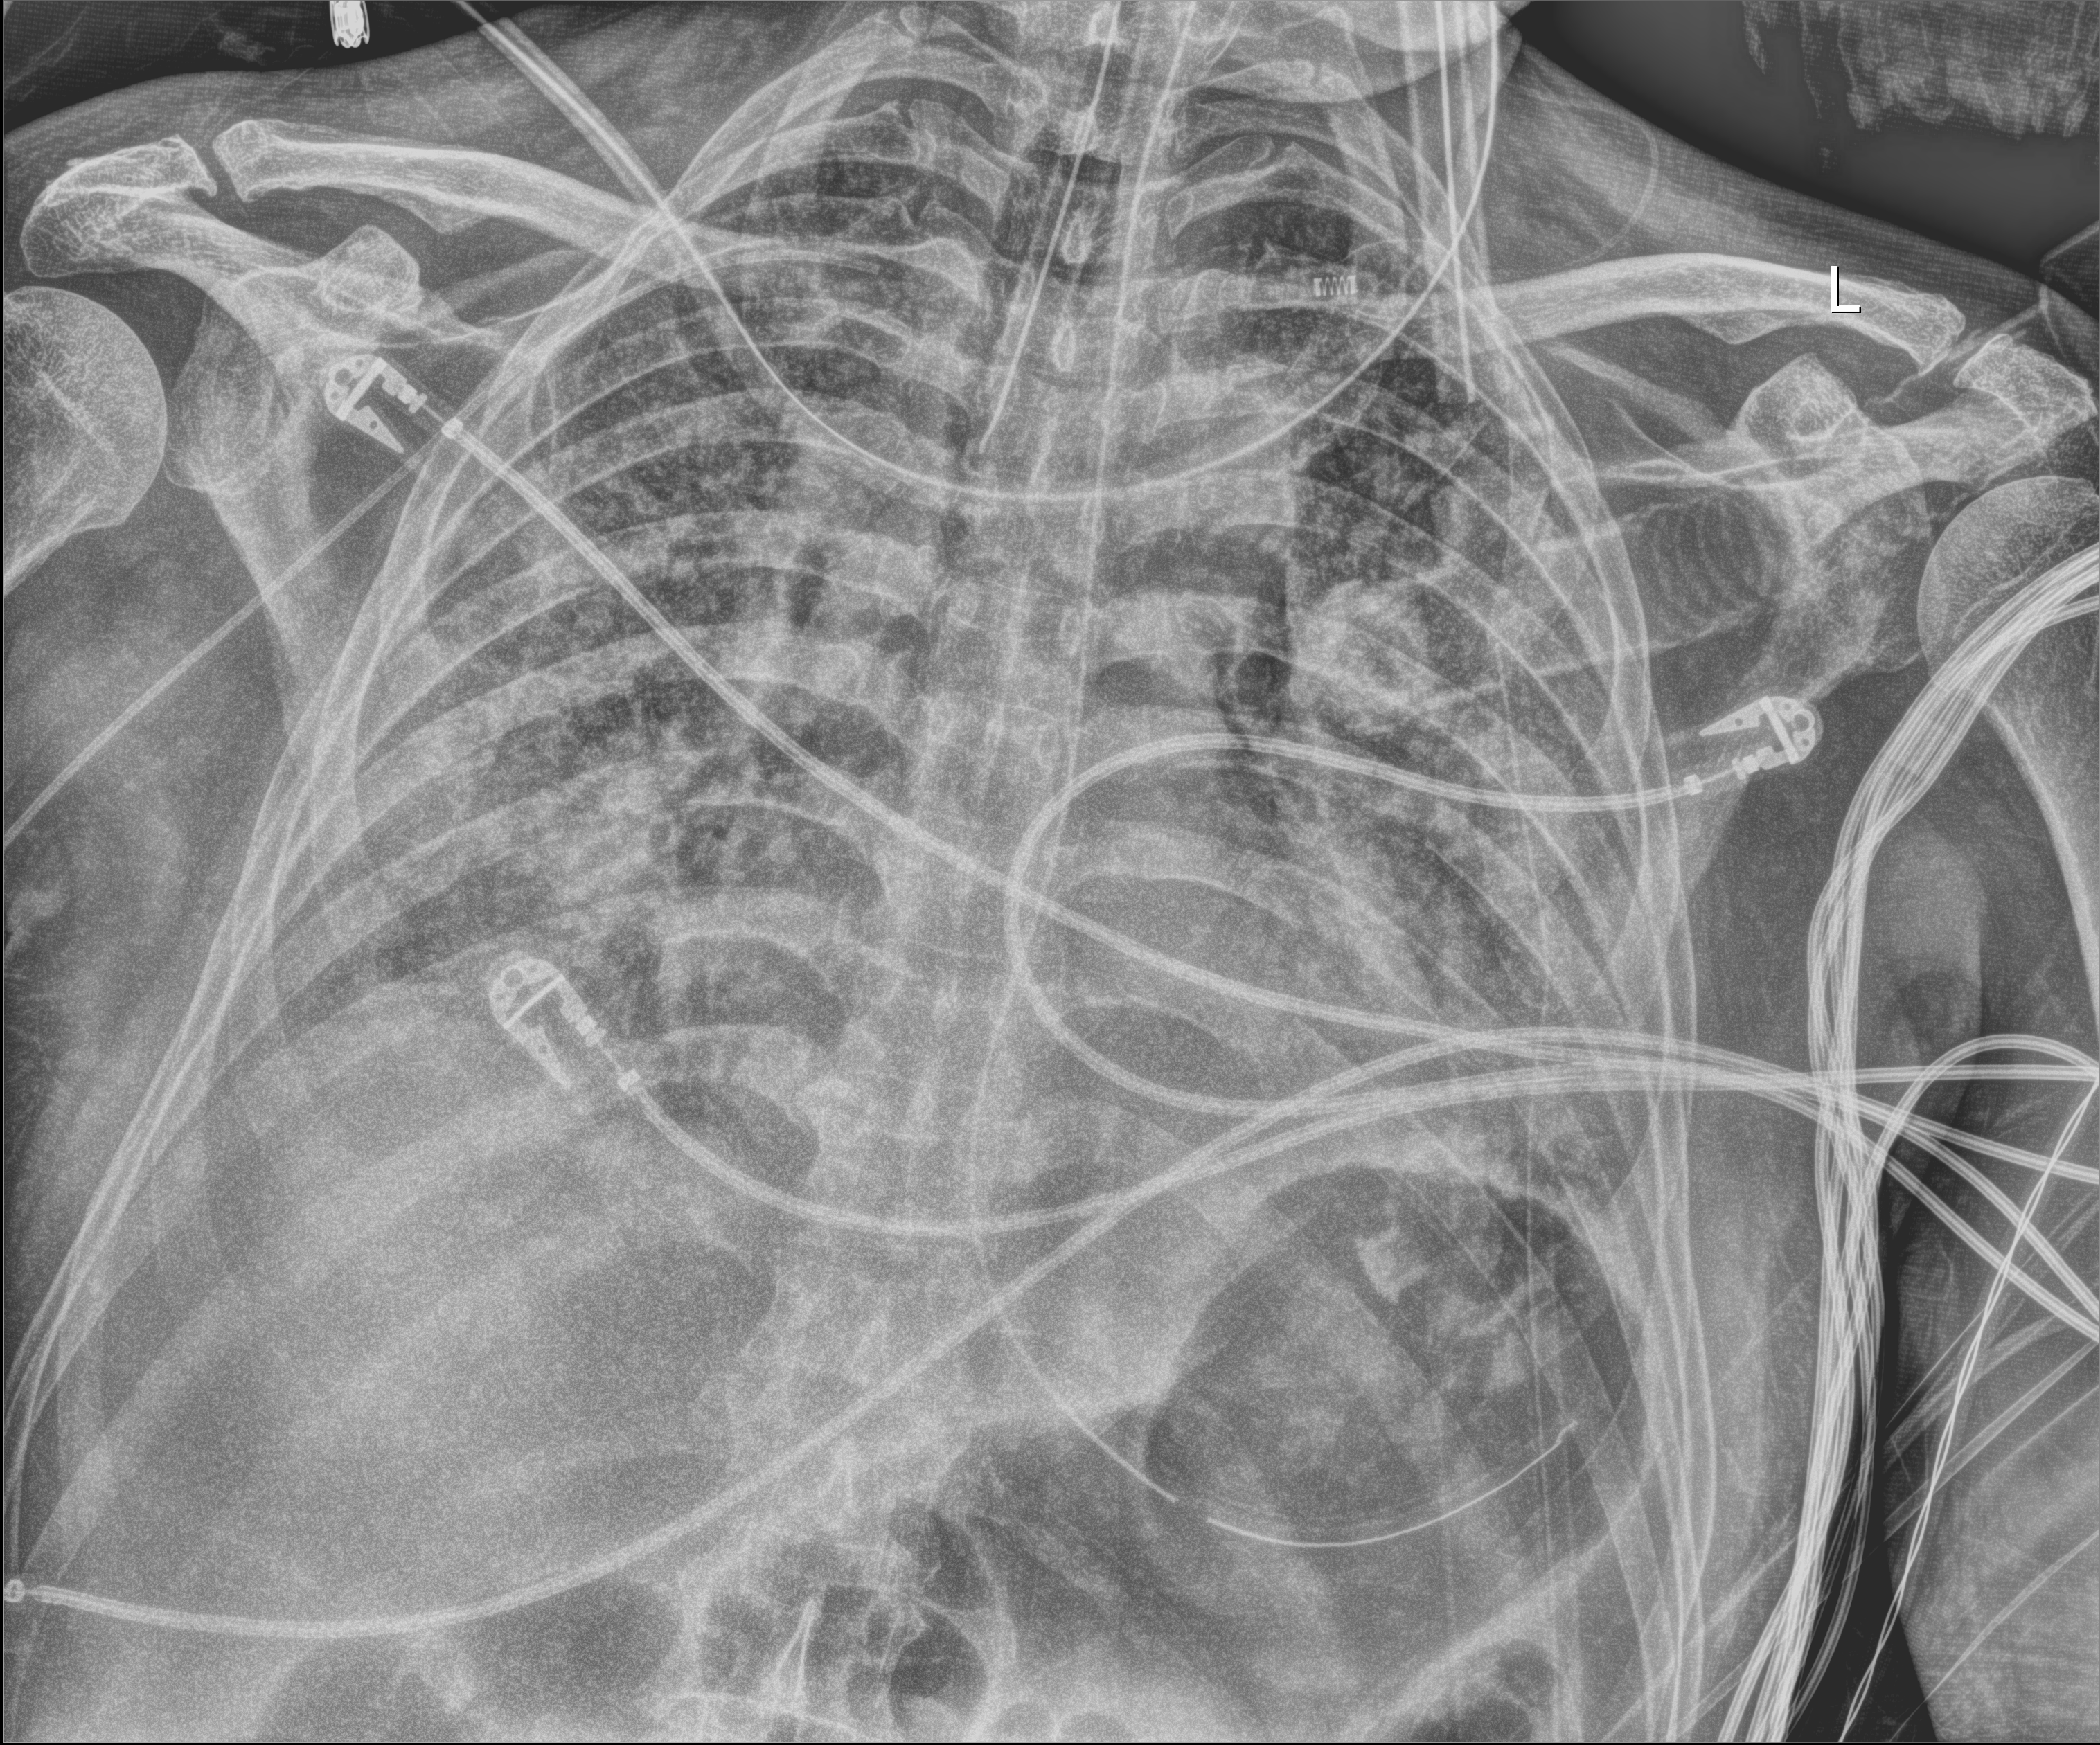
Portable chest radiograph, anteroposterior (AP) projection. Patient hospitalised with COVID-19; male, aged 60–74 years.
Hospital-stay facts (about this admission, not read from this image; timing relative to this image not recorded):
- admitted to intensive care during this hospital stay: yes
- length of hospital stay: 37 days